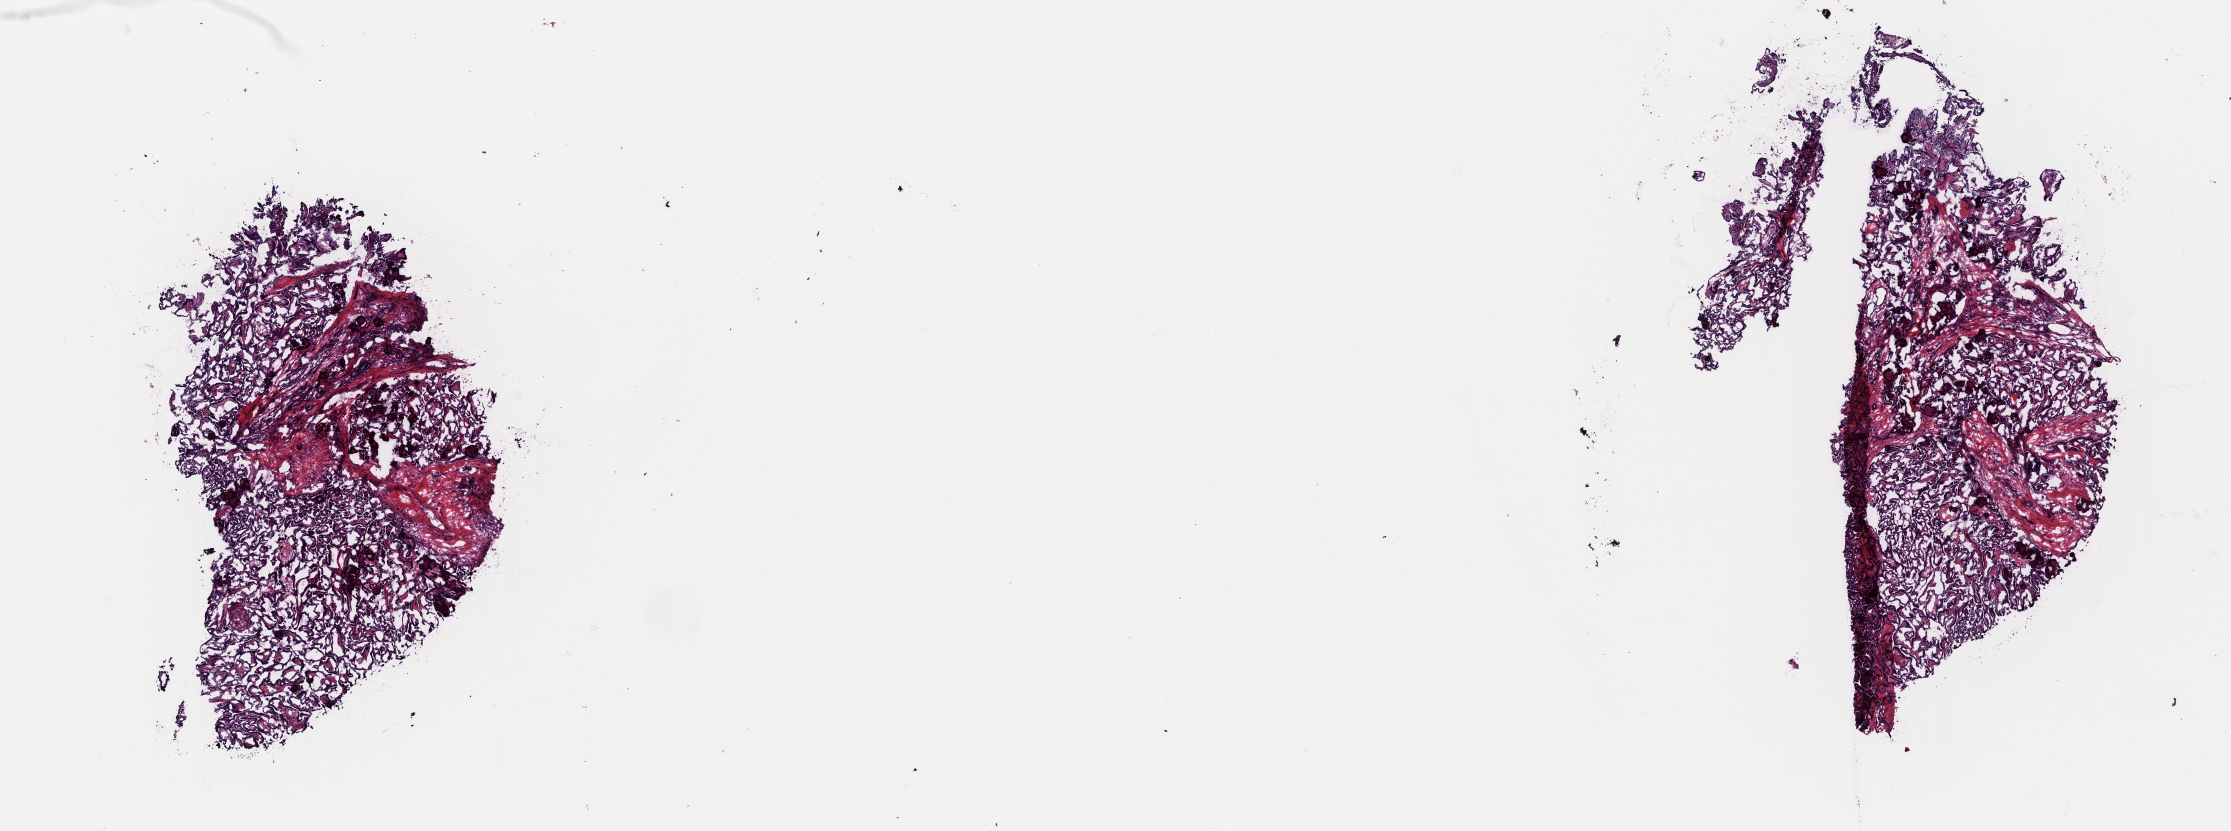
Digitized H&E-stained tissue section (whole slide), whole scanned area (about 17.6 x 6.6 mm, acquisition: 40x scan) shown as a low-resolution overview, frozen section from the top of the tissue portion, thyroid, primary tumour sample. Patient: male, age at initial diagnosis 19 years. Slide review estimates, as recorded: tumour cells 100%, tumour nuclei 75%, normal cells 0%, stromal cells 0%, necrosis 0%. Infiltration values recorded for this section: lymphocyte infiltration 0%, monocyte infiltration 0%, neutrophil infiltration 0%.
- AJCC pathologic stage: I
- lymph nodes positive (case pathology): 9 of 47 examined
- diagnosis: Papillary adenocarcinoma, NOS (thyroid gland)